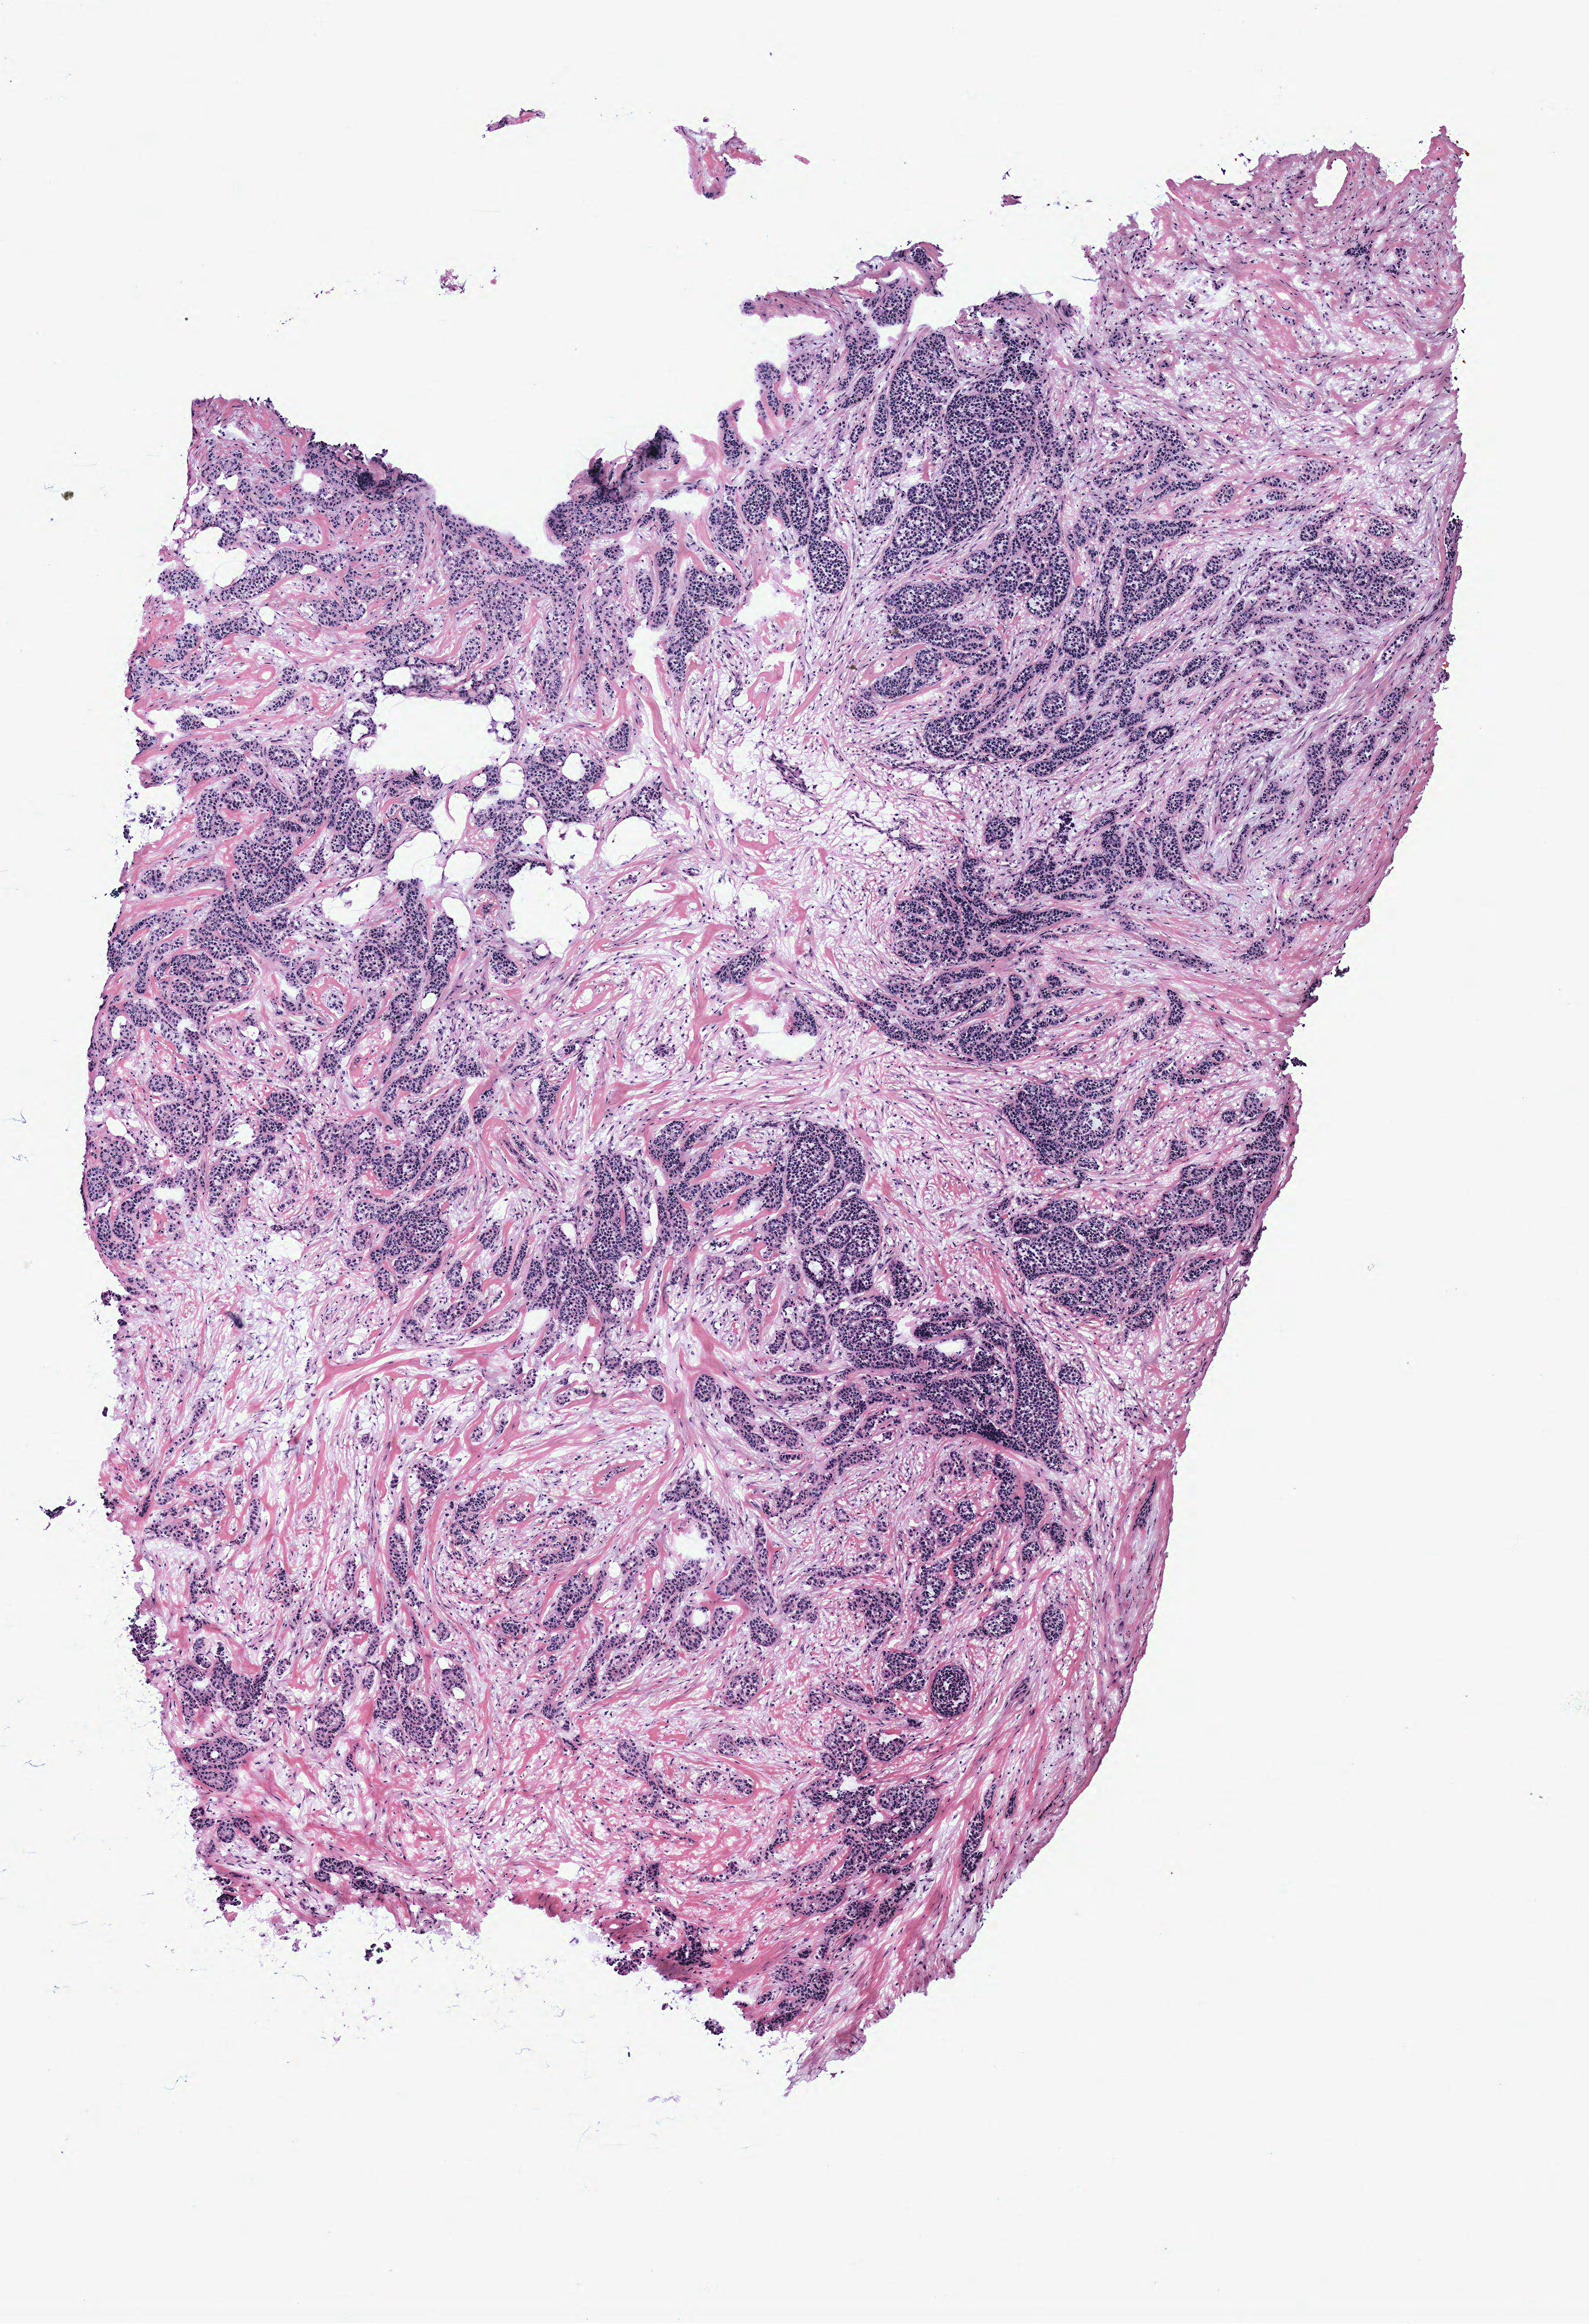
Whole-slide histology image, H&E, whole scanned area (about 4.1 x 6.0 mm, from a 40x scan) shown as a low-resolution overview, breast, tumour tissue. Female, 52 y/o.
AJCC pathologic stage: IIA. Histologic diagnosis: Infiltrating duct carcinoma, NOS.